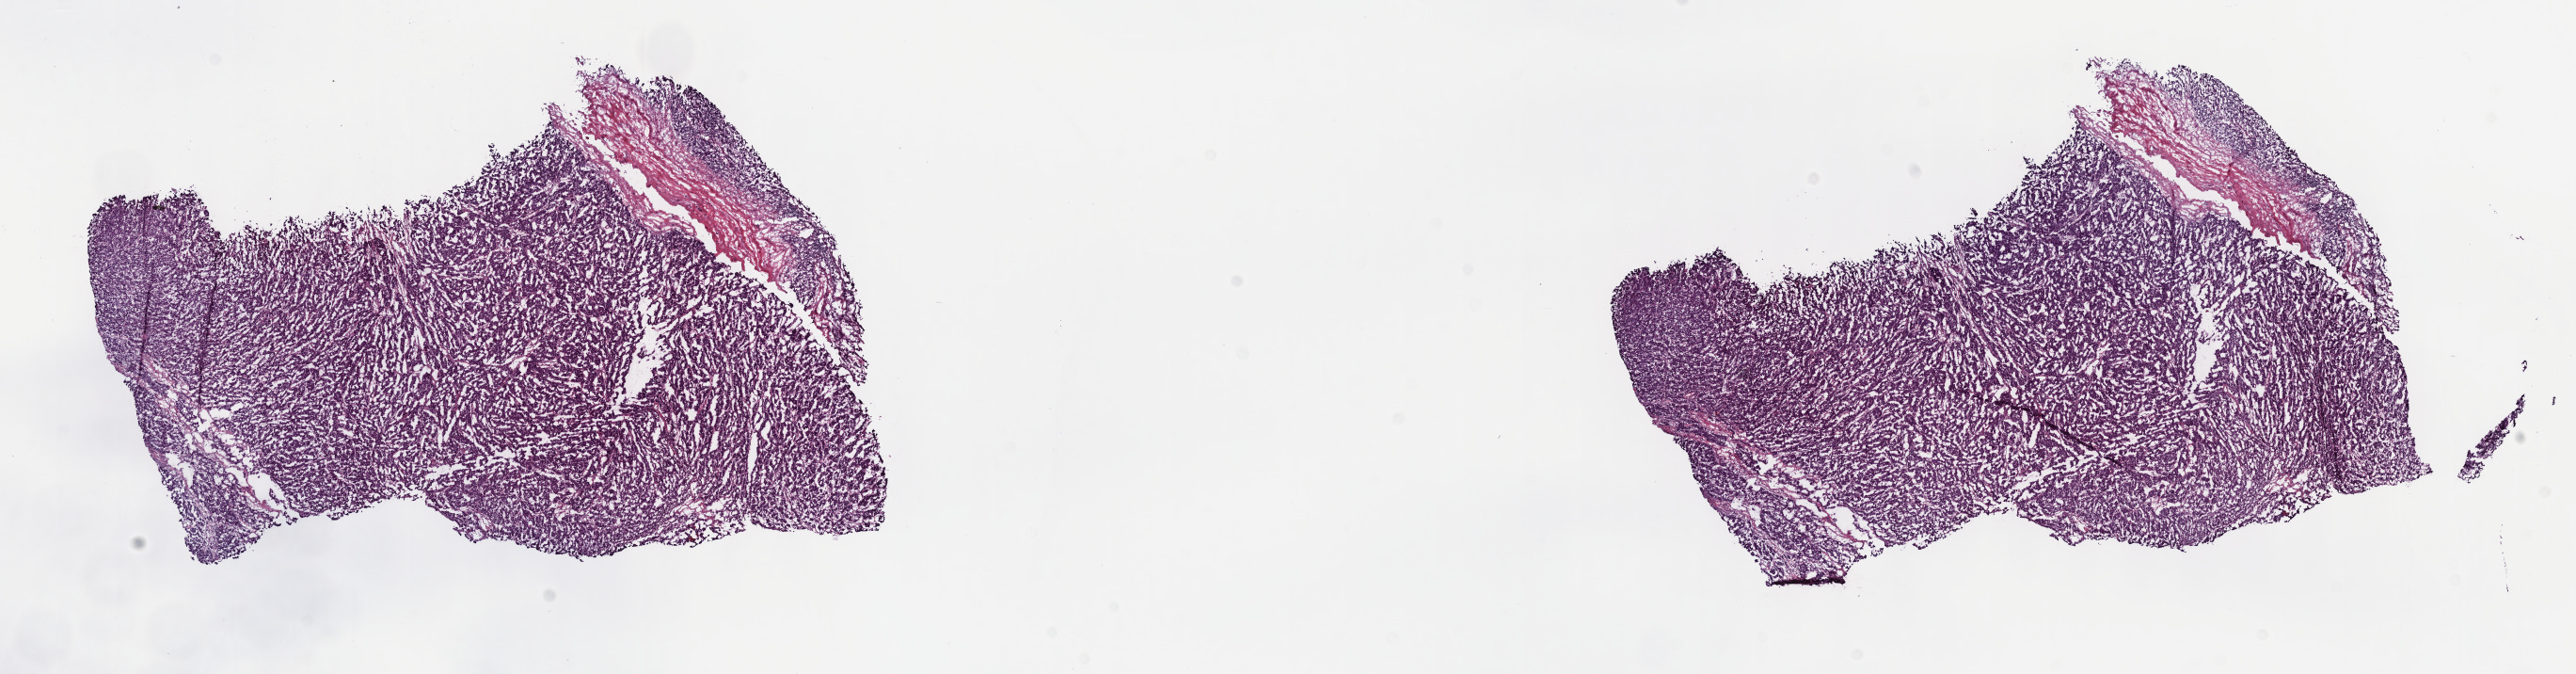
Whole-slide histology image, Hematoxylin and eosin (H&E) stained, shown as a low-resolution overview of the whole scanned area (about 22.1 x 5.8 mm). Frozen section from the top of the tissue portion. Primary tumour sample from the liver. Male, age 40 years at initial diagnosis. Histologic grade: G3 (poorly differentiated). Pathologist review of this section (percent, as recorded): tumour cells 80%, tumour nuclei 80%, normal cells 0%, stromal cells 20%, necrosis 0%. Infiltration values recorded for this section: lymphocyte infiltration 3%, monocyte infiltration 1%, neutrophil infiltration 1%.
AJCC pathologic stage: I (6th edition). Pathologic diagnosis: Hepatocellular carcinoma, NOS.